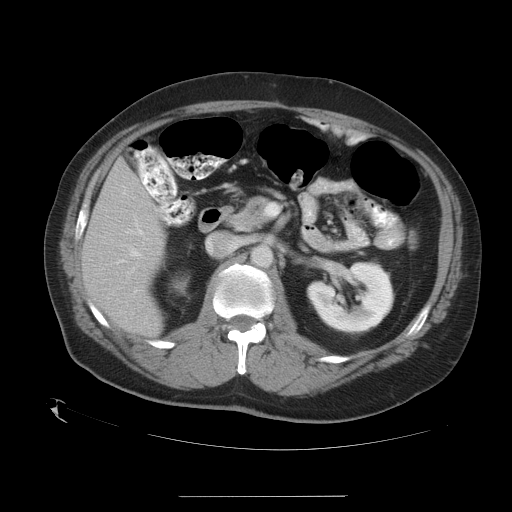
Contrast-enhanced abdominal CT, one axial slice; slice 15 of 35 in the series (ordered by position); soft-tissue window (W 400 / L 40 HU); 512 × 512 image matrix, field of view 450 × 450 mm. Male patient, age 67 years. Case-level facts recorded for this patient, not image findings: diagnosis: colorectal cancer liver metastases, imaged before liver resection; multiple liver metastases: no; largest metastasis: 2.3 cm; disease in both lobes: no.
Outlined on this slice (manually delineated by an expert):
- liver: bounding box <83,161,164,334> (left, top, right, bottom; pixels)
- planned liver remnant (the part of the liver to remain after resection): <83,161,164,334>
- portal vein (with intrahepatic branches): <126,224,146,292>